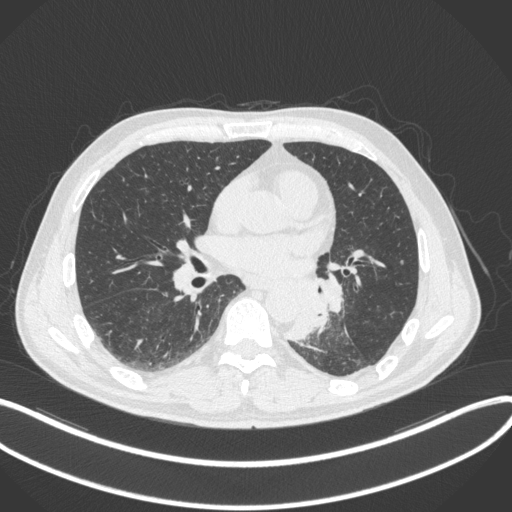
Chest CT, one axial slice; position 159 of 328 along the scan axis; reconstruction kernel B31f; 120 kVp; lung window (W 1500 / L -600 HU); 1 mm slice thickness; 512 × 512 image matrix. Patient: male, 59 years. From the clinical record (not read from this slice): clinical TNM (as recorded): T2a N2 M0.
Outlined on this slice (rectangle marked by the reading radiologist):
- lung tumour (recorded histology: squamous cell carcinoma): bounding box <282,273,346,342> (left, top, right, bottom; pixels)